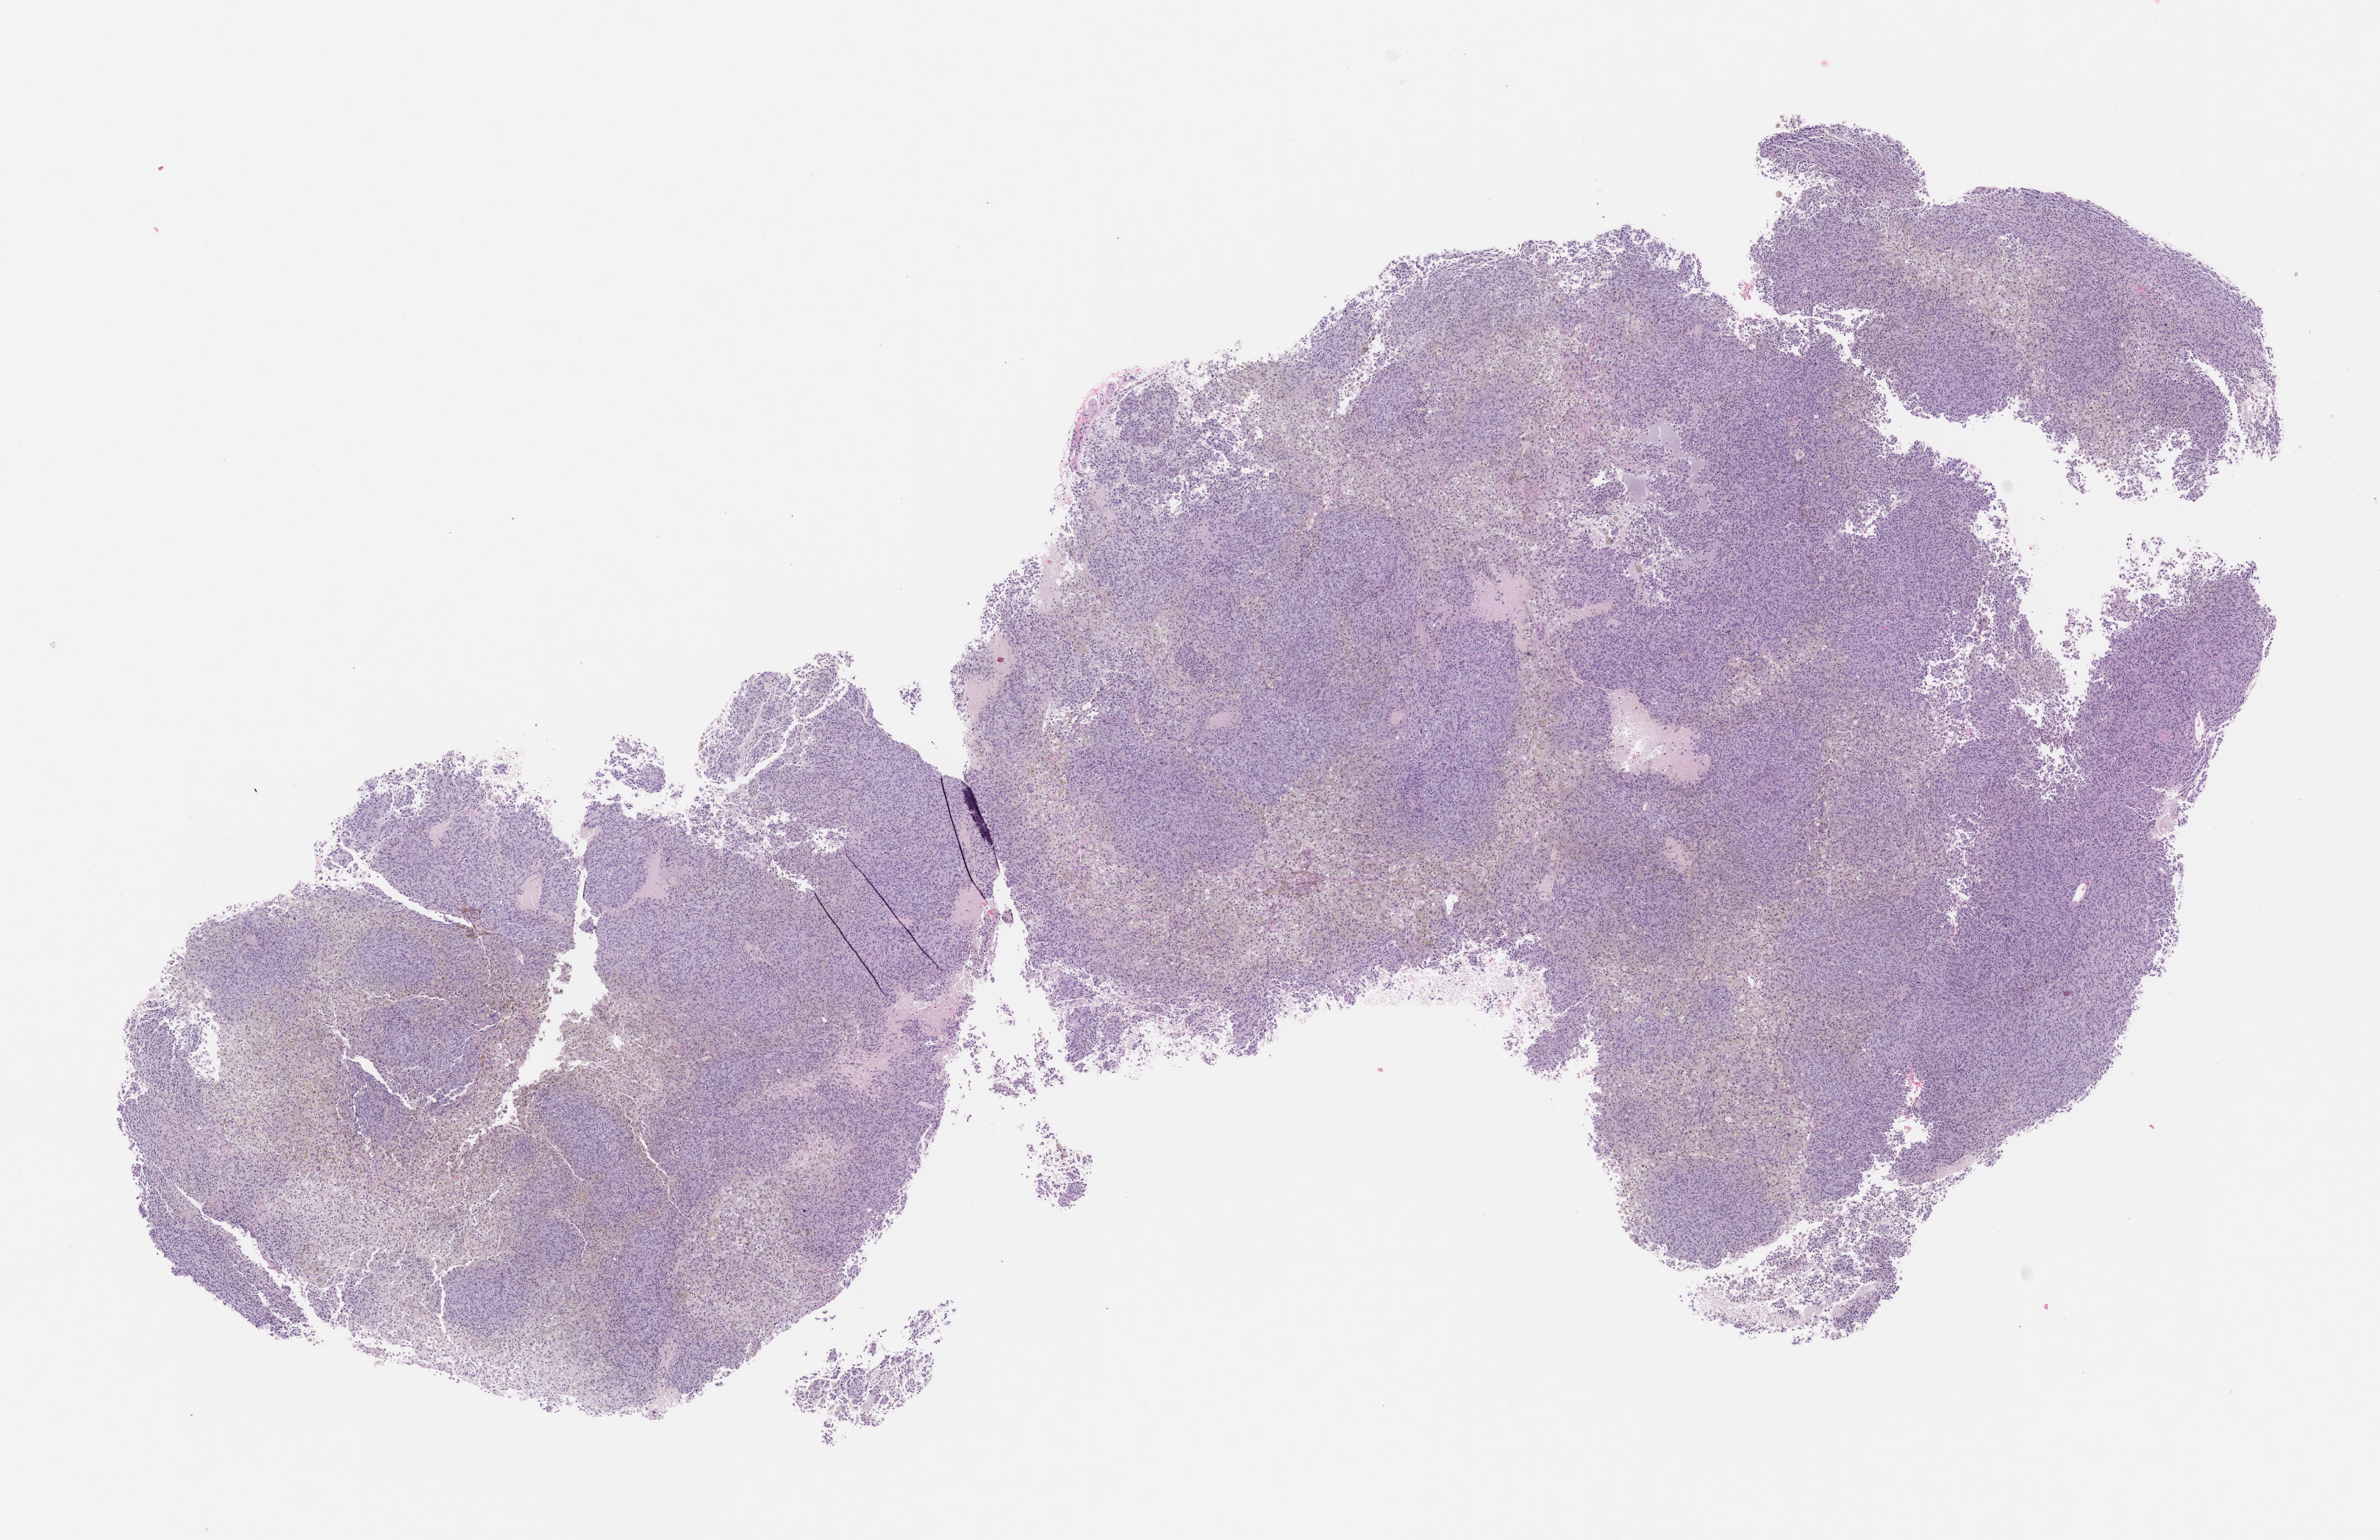
H&E whole-slide image of a patient-derived xenograft (PDX) tumor grown in a mouse, passage 0, a low-resolution overview of the entire scanned area, about 13.0 x 8.4 mm, formalin-fixed, paraffin-embedded (FFPE) tissue, tumor site category: skin.
- originating patient diagnosis: Melanoma